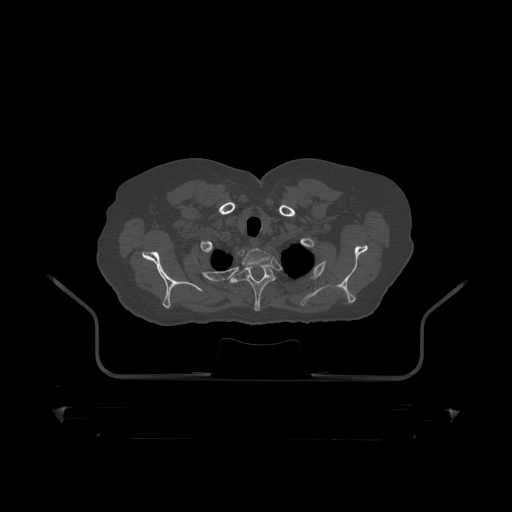
CT including the spine, one axial slice; position 378 of 390 along the scan axis; reconstruction kernel STANDARD; bone window (W 1800 / L 400 HU); 1.25 mm slice thickness; 512 × 512 image matrix. Male patient, age 60 years. Case-level facts recorded for this patient, not image findings: primary cancer: prostate.
Outlined on this slice (semi-automatically segmented with operator editing):
- T1 vertebra: bounding box (x1, y1, x2, y2) in pixels: (211, 245, 271, 267)
- T2 vertebra: (230, 263, 275, 312)